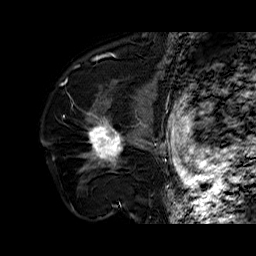
Breast MRI (dynamic contrast-enhanced), one sagittal slice. Position 43 of 60 along the scan axis. Dynamic contrast-enhanced series, time point 2 of 6 at this slice position (early post-contrast). 1.5 T. TE 6.4 ms, TR 32.7 ms. 256 × 256 image matrix, field of view 200 × 200 mm. Female patient. Case-level facts recorded for this patient, not image findings: setting: breast cancer imaged before/during neoadjuvant chemotherapy; receptor status: HR-positive, HER2-negative.
Outlined on this slice (semi-automatic segmentation, software-assisted and operator-edited):
- analysis volume of interest (the breast-tissue region the enhancement analysis was run in; not a lesion): box from (x=79, y=110) to (x=141, y=174) px
- tumour enhancement mask (voxels above the 100 % enhancement threshold inside the analysis volume of interest): (x=88, y=119)–(x=125, y=165)